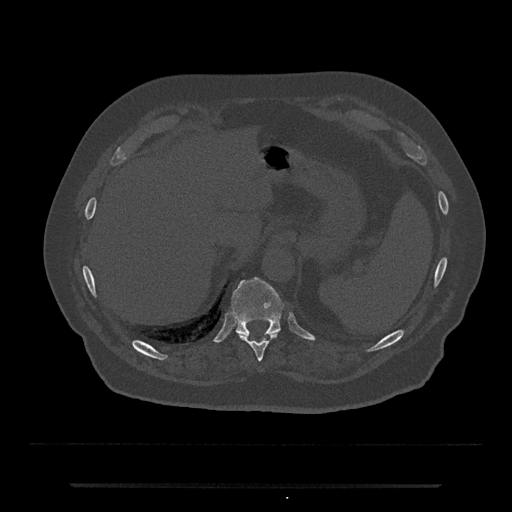
CT including the spine, one axial slice; slice 678 of 797 in the series (ordered by position); reconstruction kernel Br40s/3; bone window (W 1800 / L 400 HU); 0.5 mm slice thickness; 512 × 512 image matrix. Male patient, age 80 years. Case-level facts recorded for this patient, not image findings: primary cancer: prostate; vertebrae with lytic lesions (as recorded): L1, T11.
Structures marked on this image (semi-automatic segmentation, software-assisted and operator-edited):
- T10 vertebra: bounding box <239,333,278,362> (left, top, right, bottom; pixels)
- T11 vertebra: <232,277,284,337>